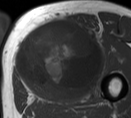
MRI of an extremity soft-tissue mass, one axial slice; slice 40 of 55 in the series (ordered by position); MR volume resampled by the dataset authors to the PET/CT grid (not the native acquisition matrix); 3.27 mm slice thickness; 131 × 118 image matrix, field of view 128 × 115 mm. Male patient. Case-level facts recorded for this patient, not image findings: histological type: pleiomorphic liposarcoma; grade: high; site of the primary tumour: left thigh.
Annotated regions visible in this slice (expert contour drawn on MRI and transferred to this co-registered scan by the dataset authors):
- gross tumour volume including surrounding oedema: bounding box <16,20,104,95> (left, top, right, bottom; pixels)
- gross tumour volume (mass): <16,20,101,95>